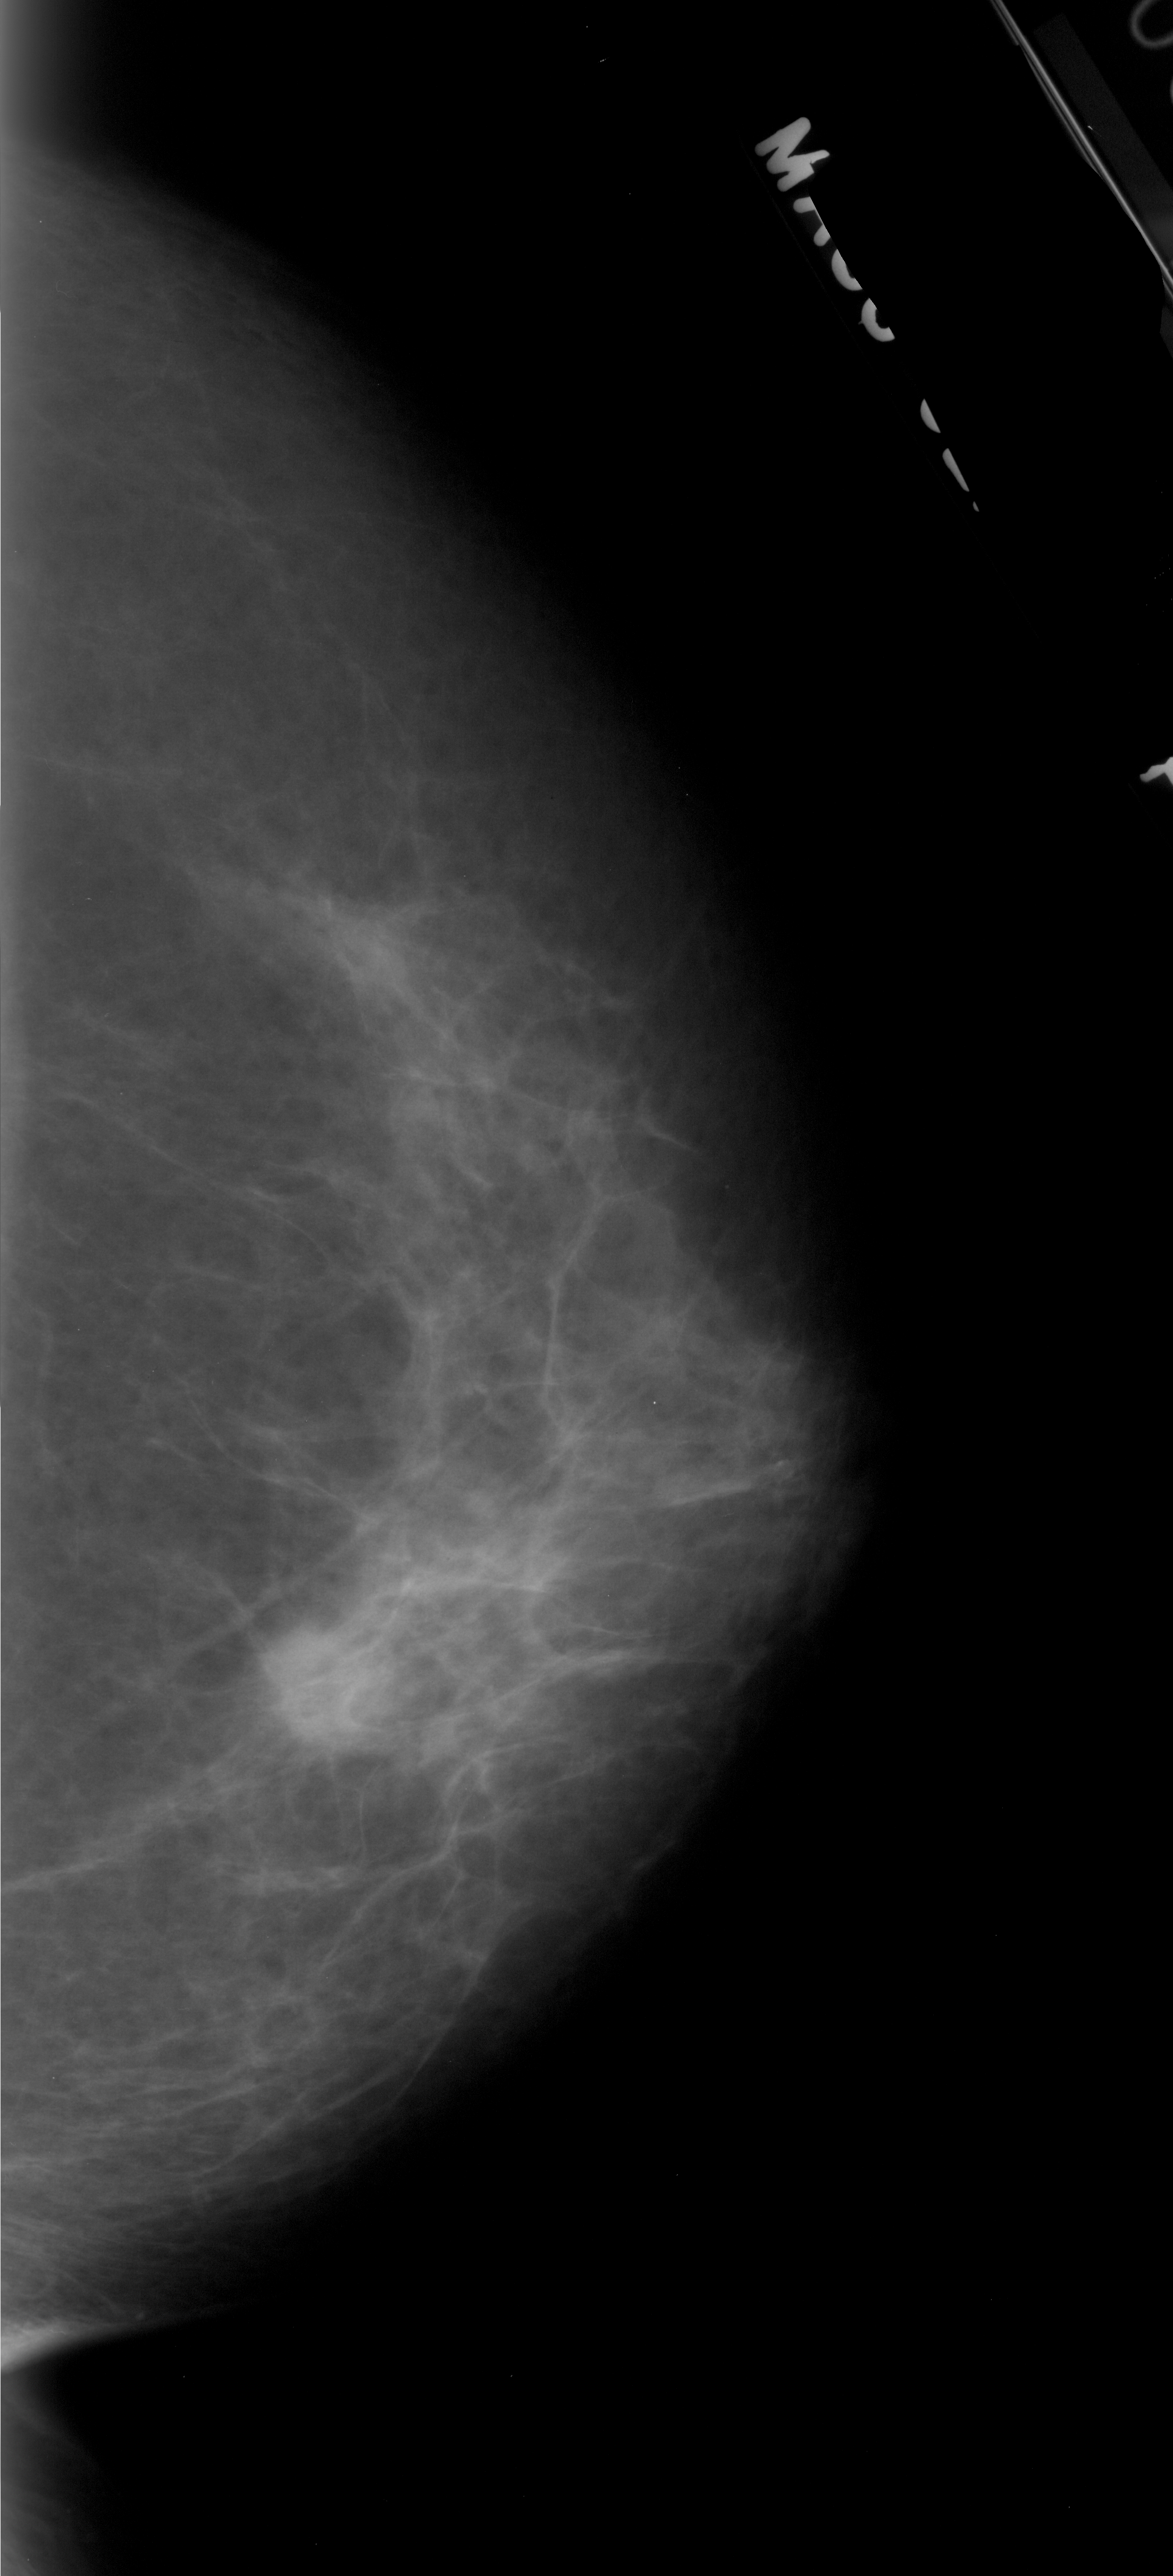
Mammogram (digitized film). Right breast. CC view. BI-RADS breast density category 2 (scale 1–4). 1173 × 2576 image matrix.
Marked abnormalities (boxes around the expert regions of interest):
- mass, shape lobulated, margins ill defined; BI-RADS assessment category 4; pathology result (as recorded, not read from the image): malignant: box from (x=257, y=1627) to (x=404, y=1760) px